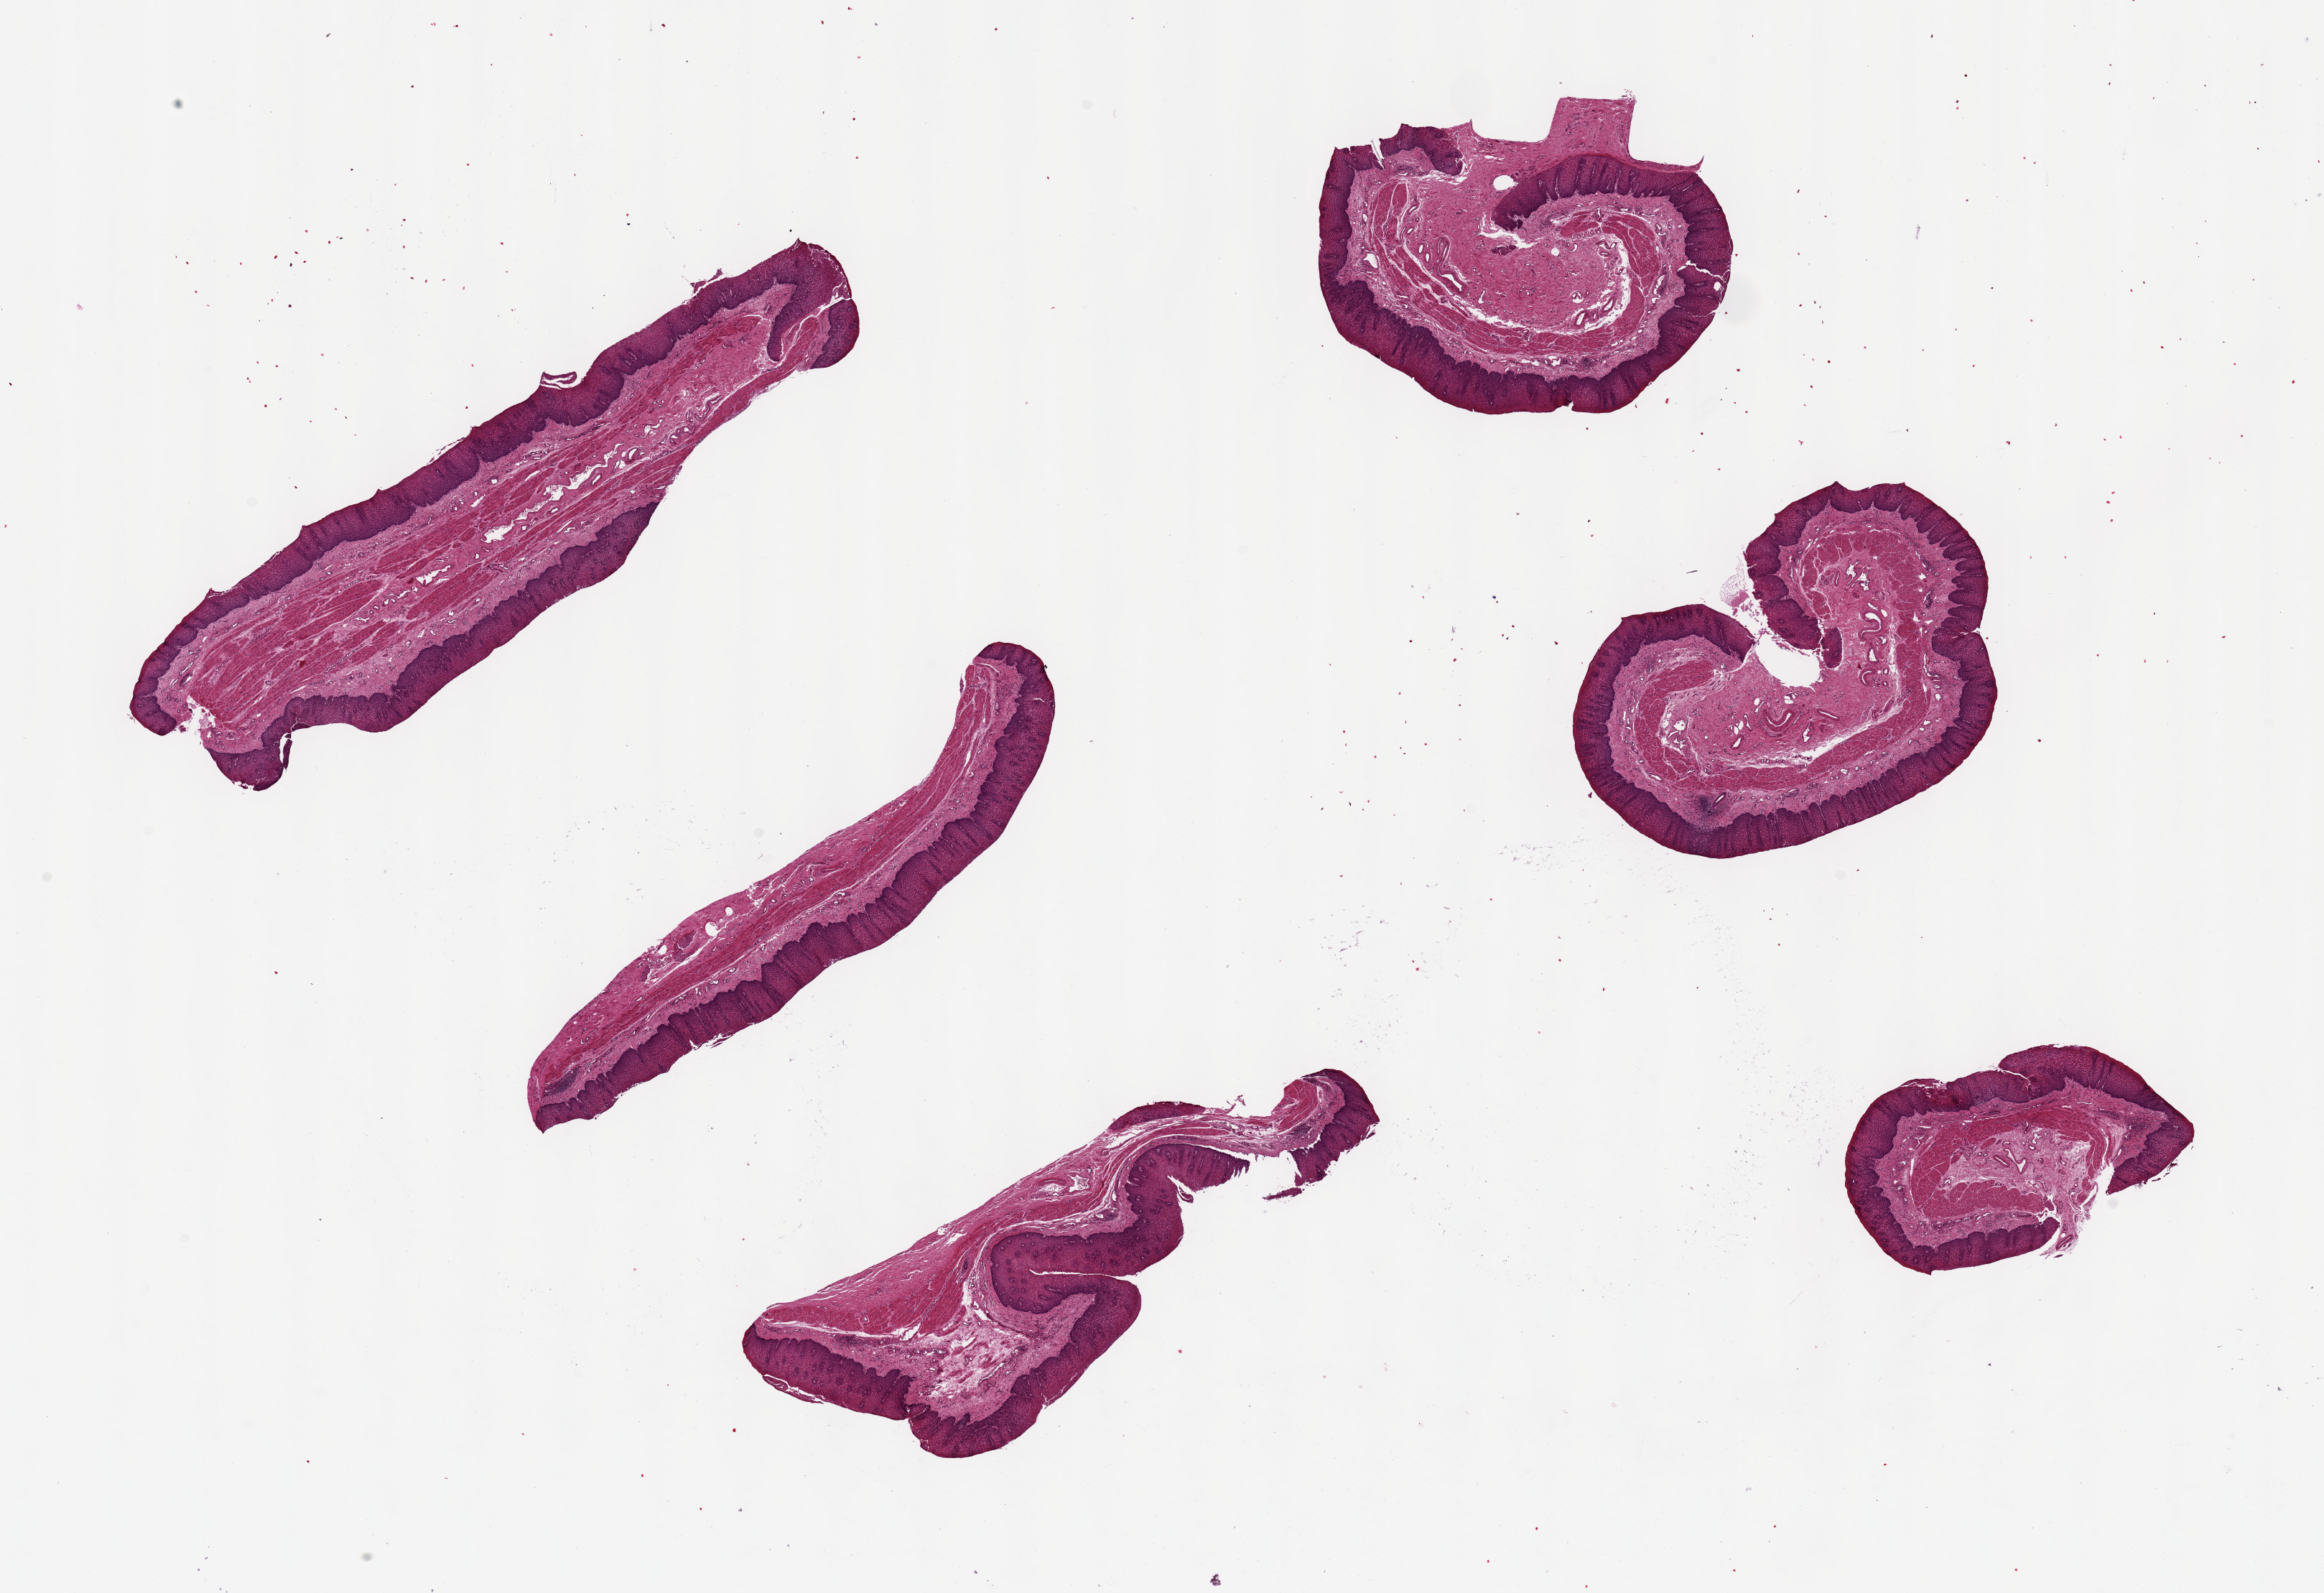
Whole-slide image, hematoxylin and eosin (H&E) stain, brightfield, whole scanned area (about 25.6 x 17.5 mm, slide scanned at 20x) shown as a low-resolution overview, PAXgene-fixed paraffin-embedded (PFPE) section, target tissue: esophageal mucous membrane, donor tissue sample. Donor sex: male.
* pathologist's review note for this sample: 6 pieces all muscularis, ~7x3mm